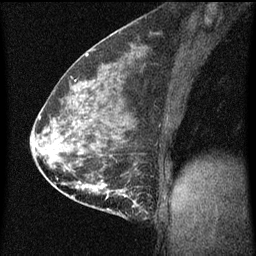
Breast MRI (dynamic contrast-enhanced), one sagittal slice. Slice 30 of 60 in the series (ordered by position). Dynamic contrast-enhanced series, image 2 of 3 at this slice position (ordered by acquisition). 1.5 T. TE 4.2 ms, TR 8 ms. 256 × 256 image matrix, field of view 180 × 180 mm. Female patient, age 35 years.
Annotated regions visible in this slice (semi-automatically segmented with operator editing):
- analysis volume of interest (the breast-tissue region the enhancement analysis was run in; not a lesion): box from (x=110, y=180) to (x=156, y=219) px
- tumour enhancement mask (voxels above the 70 % enhancement threshold inside the analysis volume of interest): (x=110, y=190)–(x=148, y=213)